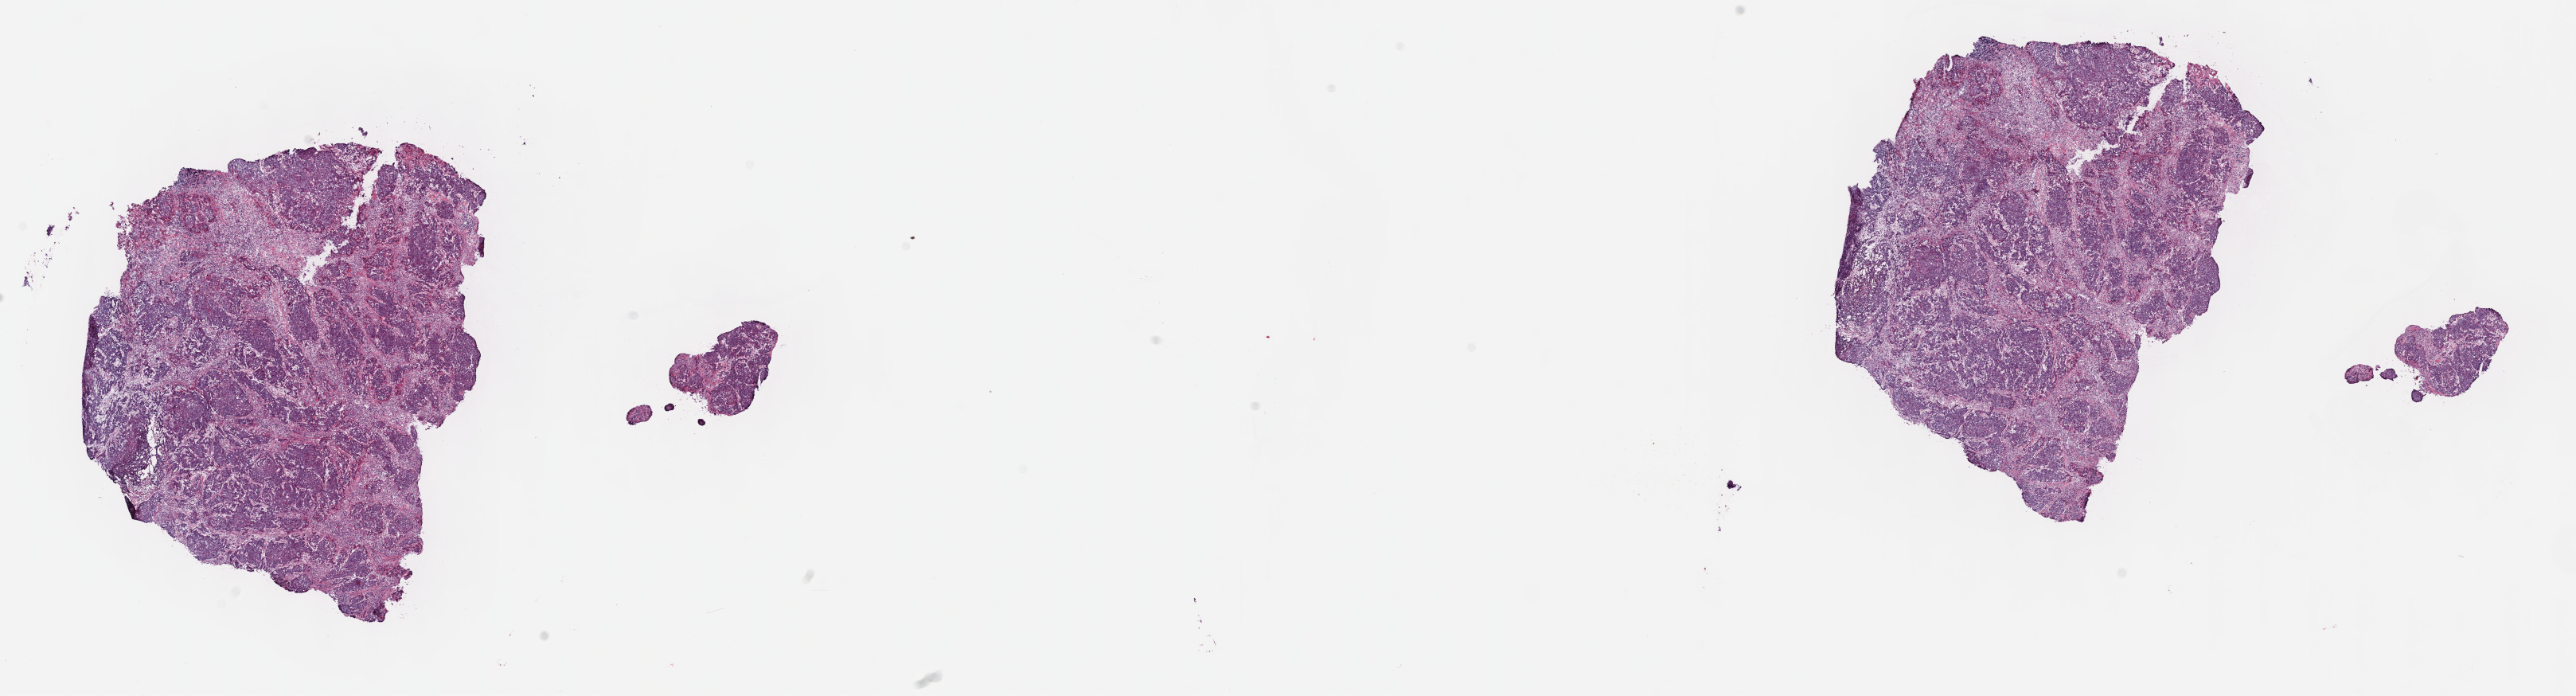
H&E whole-slide image — a low-resolution overview of the entire scanned area, about 26.2 x 7.1 mm (from a 40x scan); frozen section; metastatic tumour sample, sampled site not recorded. Female patient; age at initial diagnosis 44 years. Slide review estimates, as recorded: tumour cells 80%, tumour nuclei 80%, normal cells 0%, stromal cells 20%, necrosis 0%. Inflammatory infiltration, as recorded: lymphocyte infiltration 40%, monocyte infiltration 20%, neutrophil infiltration 20%.
This section: metastatic tumour tissue. Patient diagnosis: Squamous cell carcinoma, NOS (primary site: cervix uteri).